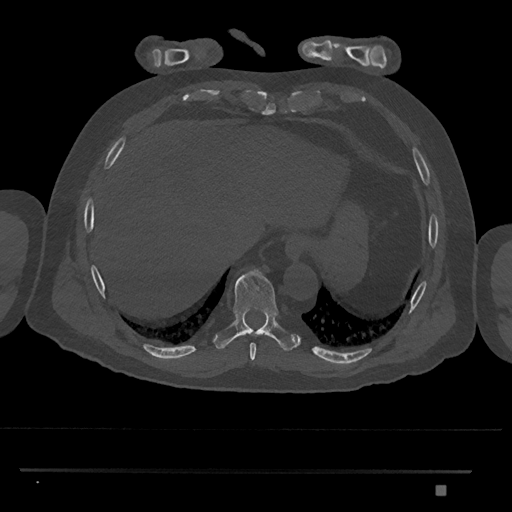
CT including the spine, one axial slice. Position 1066 of 1134 along the scan axis. Reconstruction kernel Br40s/3. 120 kVp. Bone window (W 1800 / L 400 HU). 0.5 mm slice thickness. 512 × 512 image matrix, field of view 429 × 429 mm. Male patient, age 65 years. From the clinical record (not read from this slice): primary cancer: prostate.
Structures marked on this image (semi-automatically segmented with operator editing):
- T8 vertebra: box from (x=250, y=343) to (x=256, y=361) px
- T9 vertebra: (x=215, y=269)–(x=298, y=351)